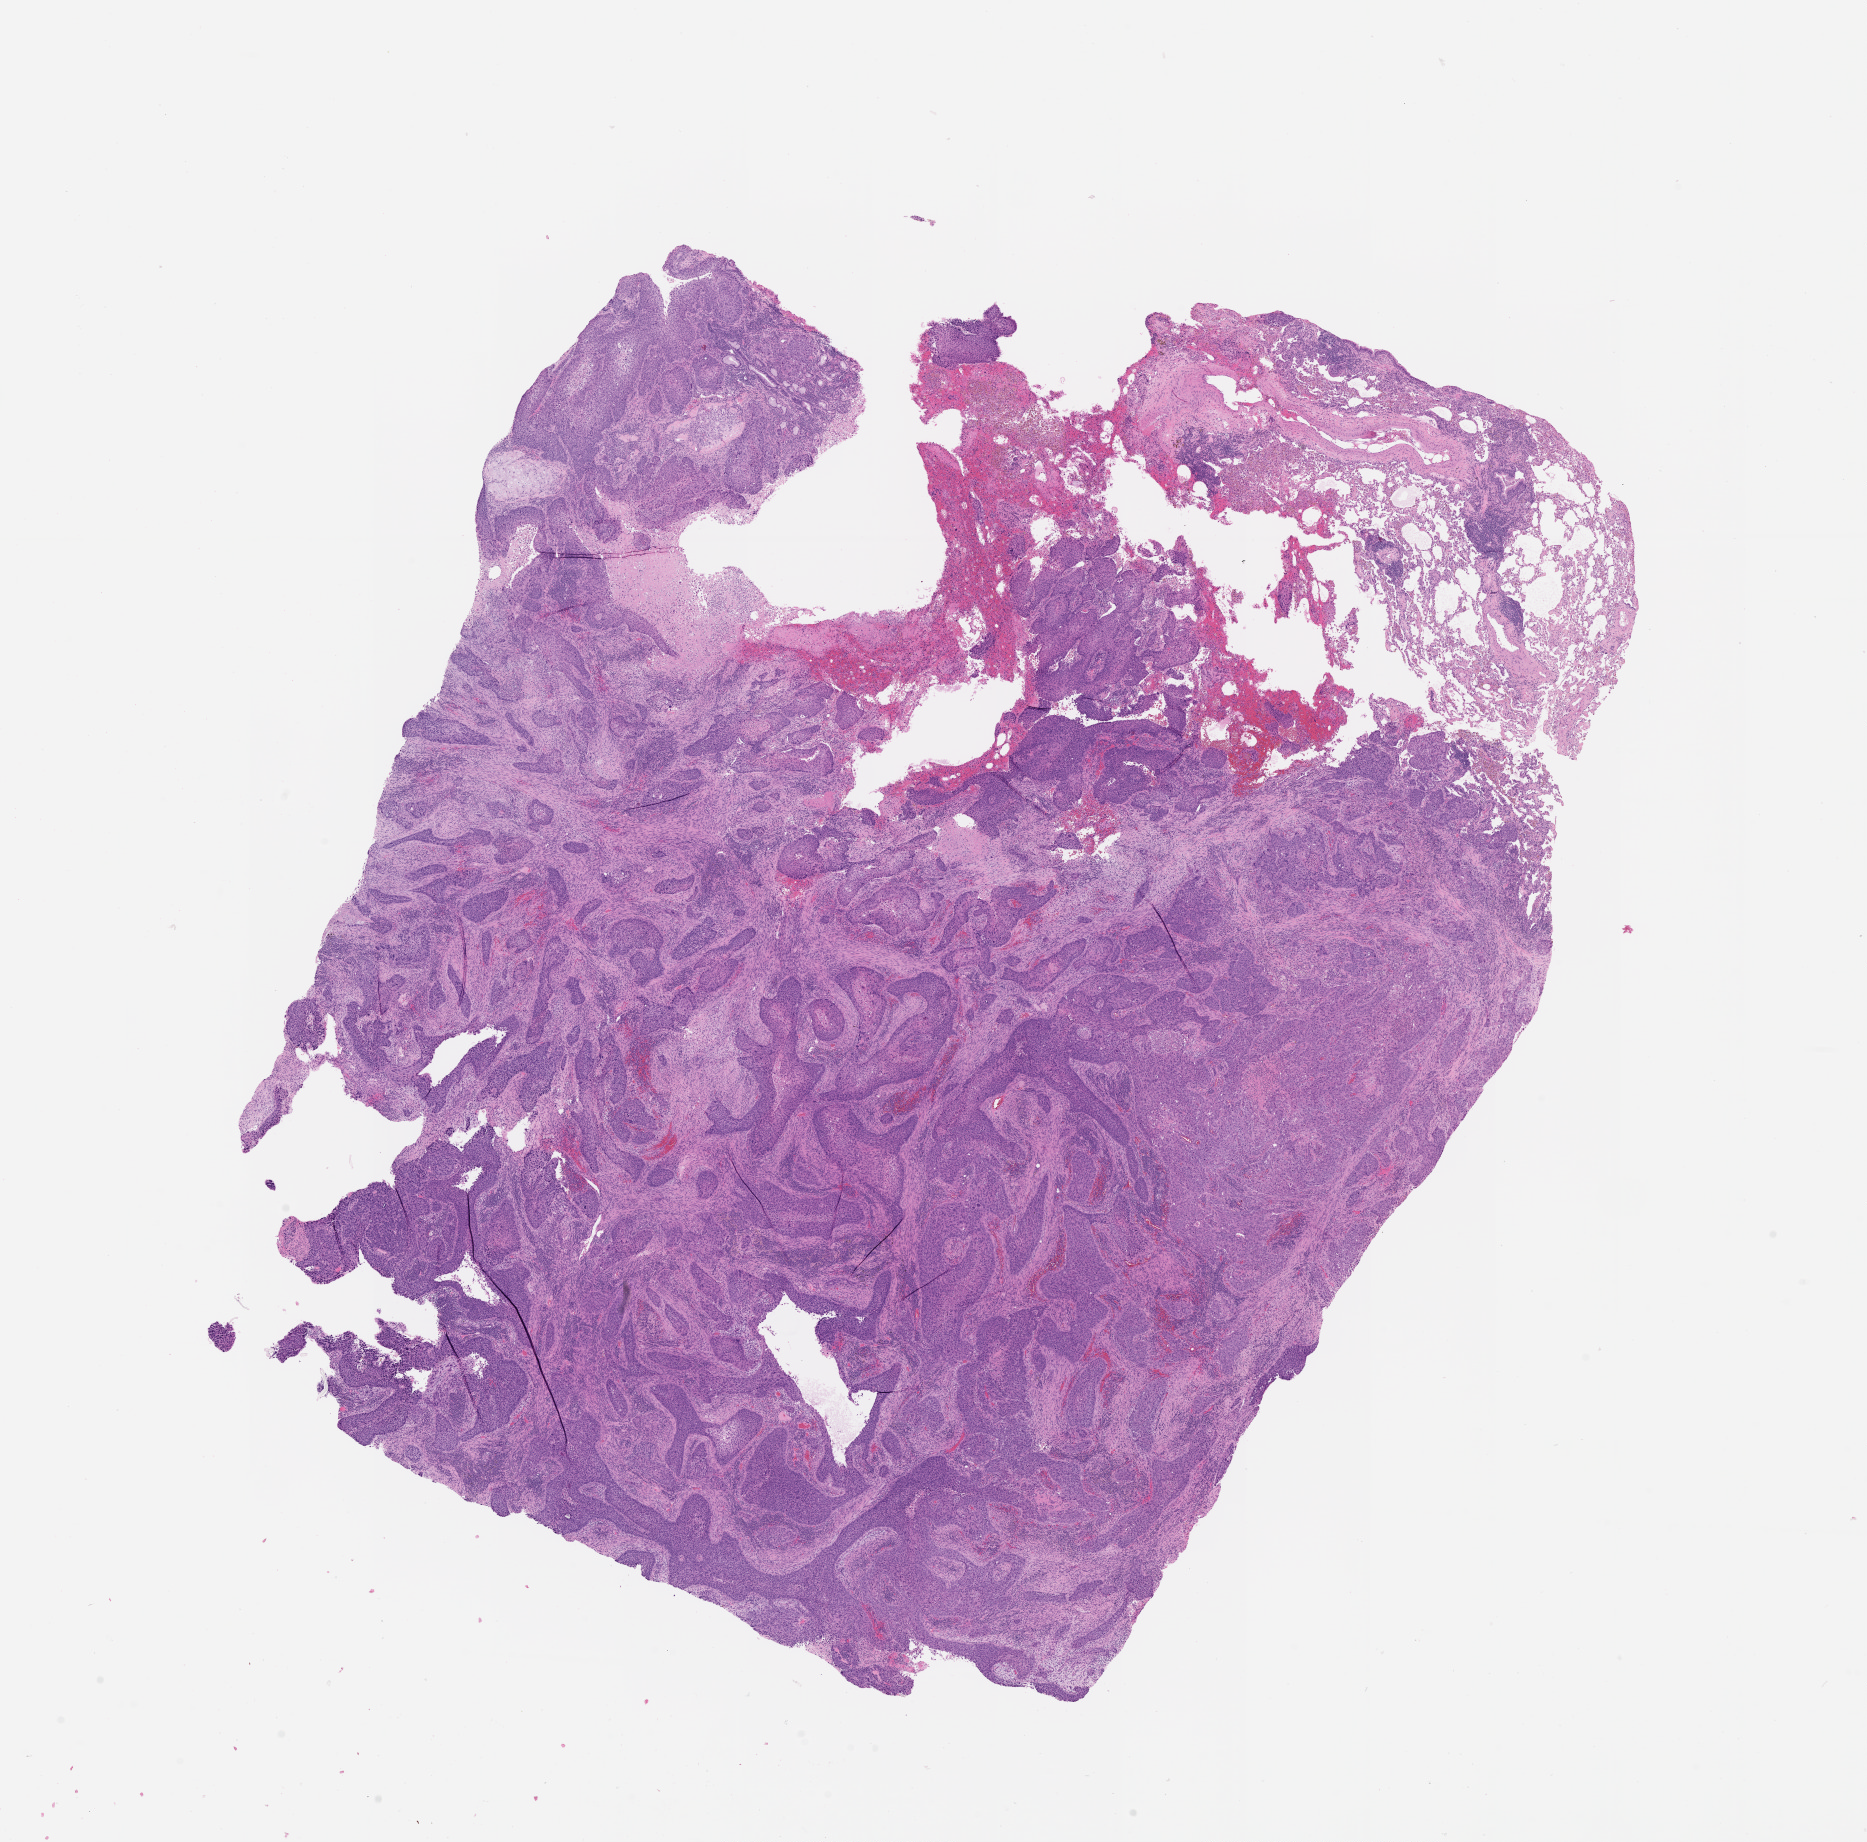
Hematoxylin and eosin (H&E) stained whole-slide image — whole scanned area (about 15.0 x 14.8 mm, from a 20x scan) shown as a low-resolution overview; tumour tissue sample, lung. 54-year-old female patient.
Patient diagnosis (cohort enrolment): squamous cell carcinoma (lung).